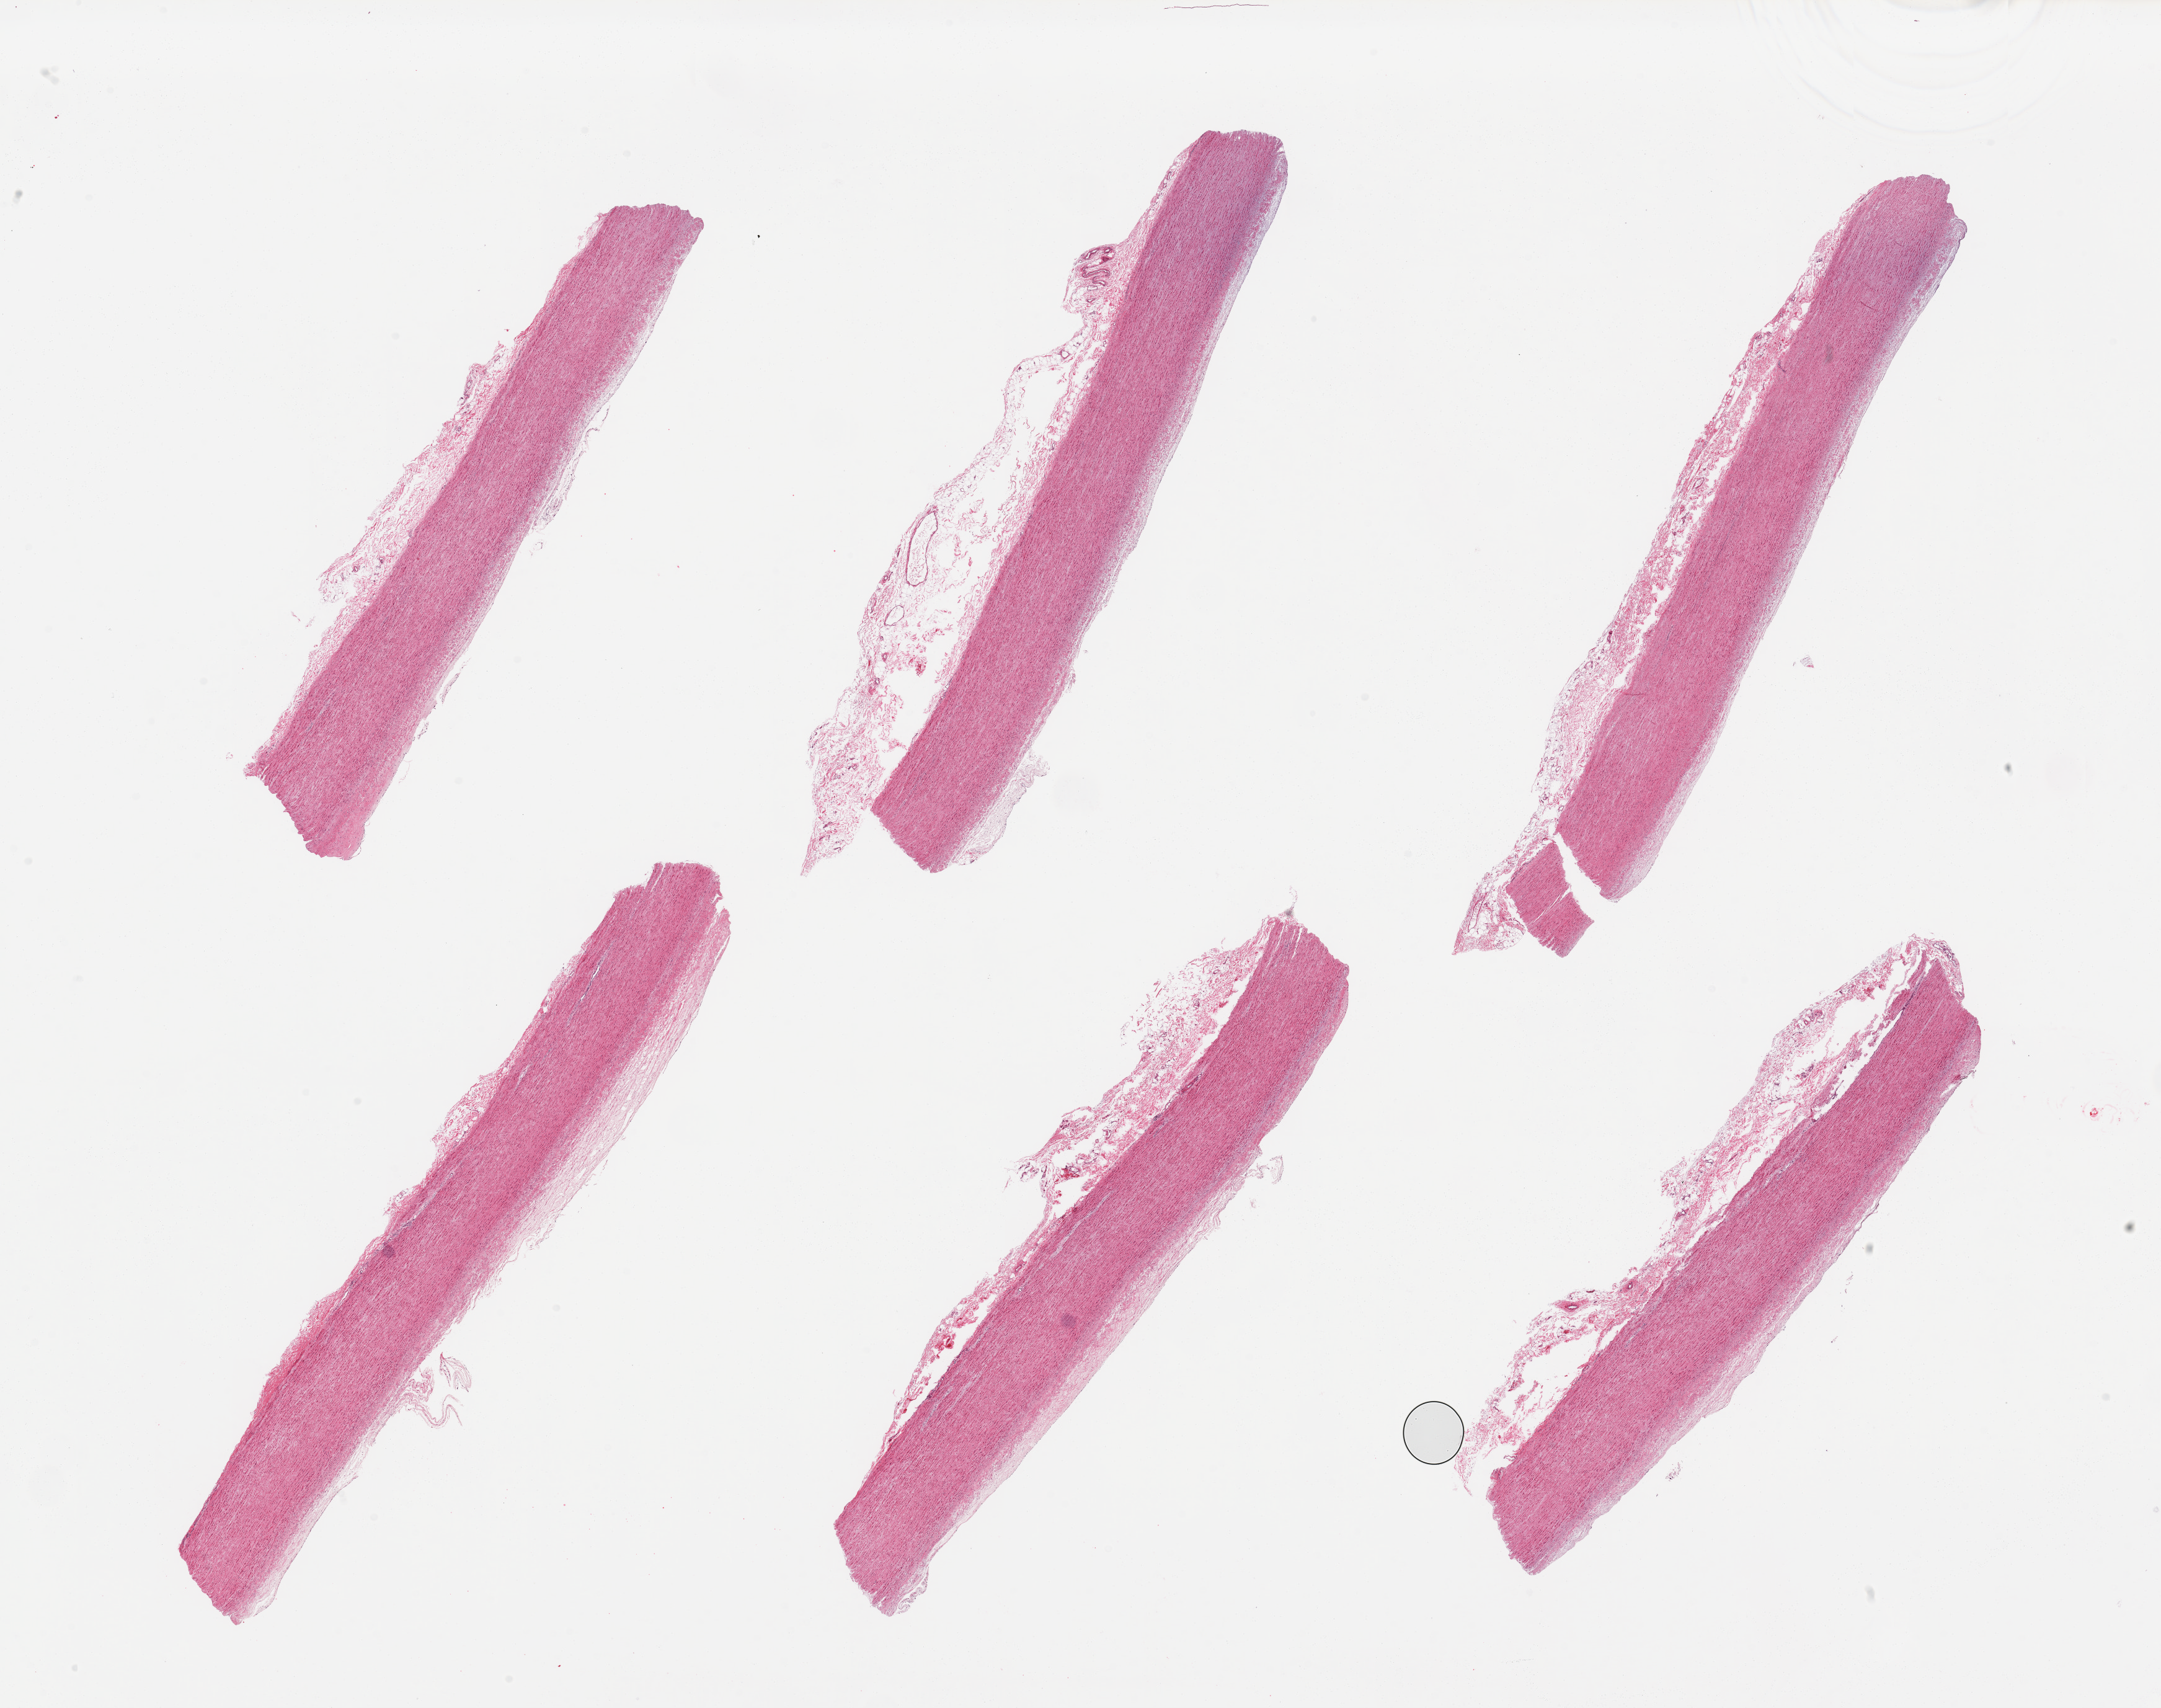
H&E whole-slide image — whole scanned area (about 27.6 x 21.8 mm) shown as a low-resolution overview, PAXgene-fixed, paraffin-embedded tissue, target tissue: aorta, tissue donor sample. Male donor.
Reviewer comment on this tissue sample: 6 pieces; minimal plaque; adventitial stroma up to 1mm thick.